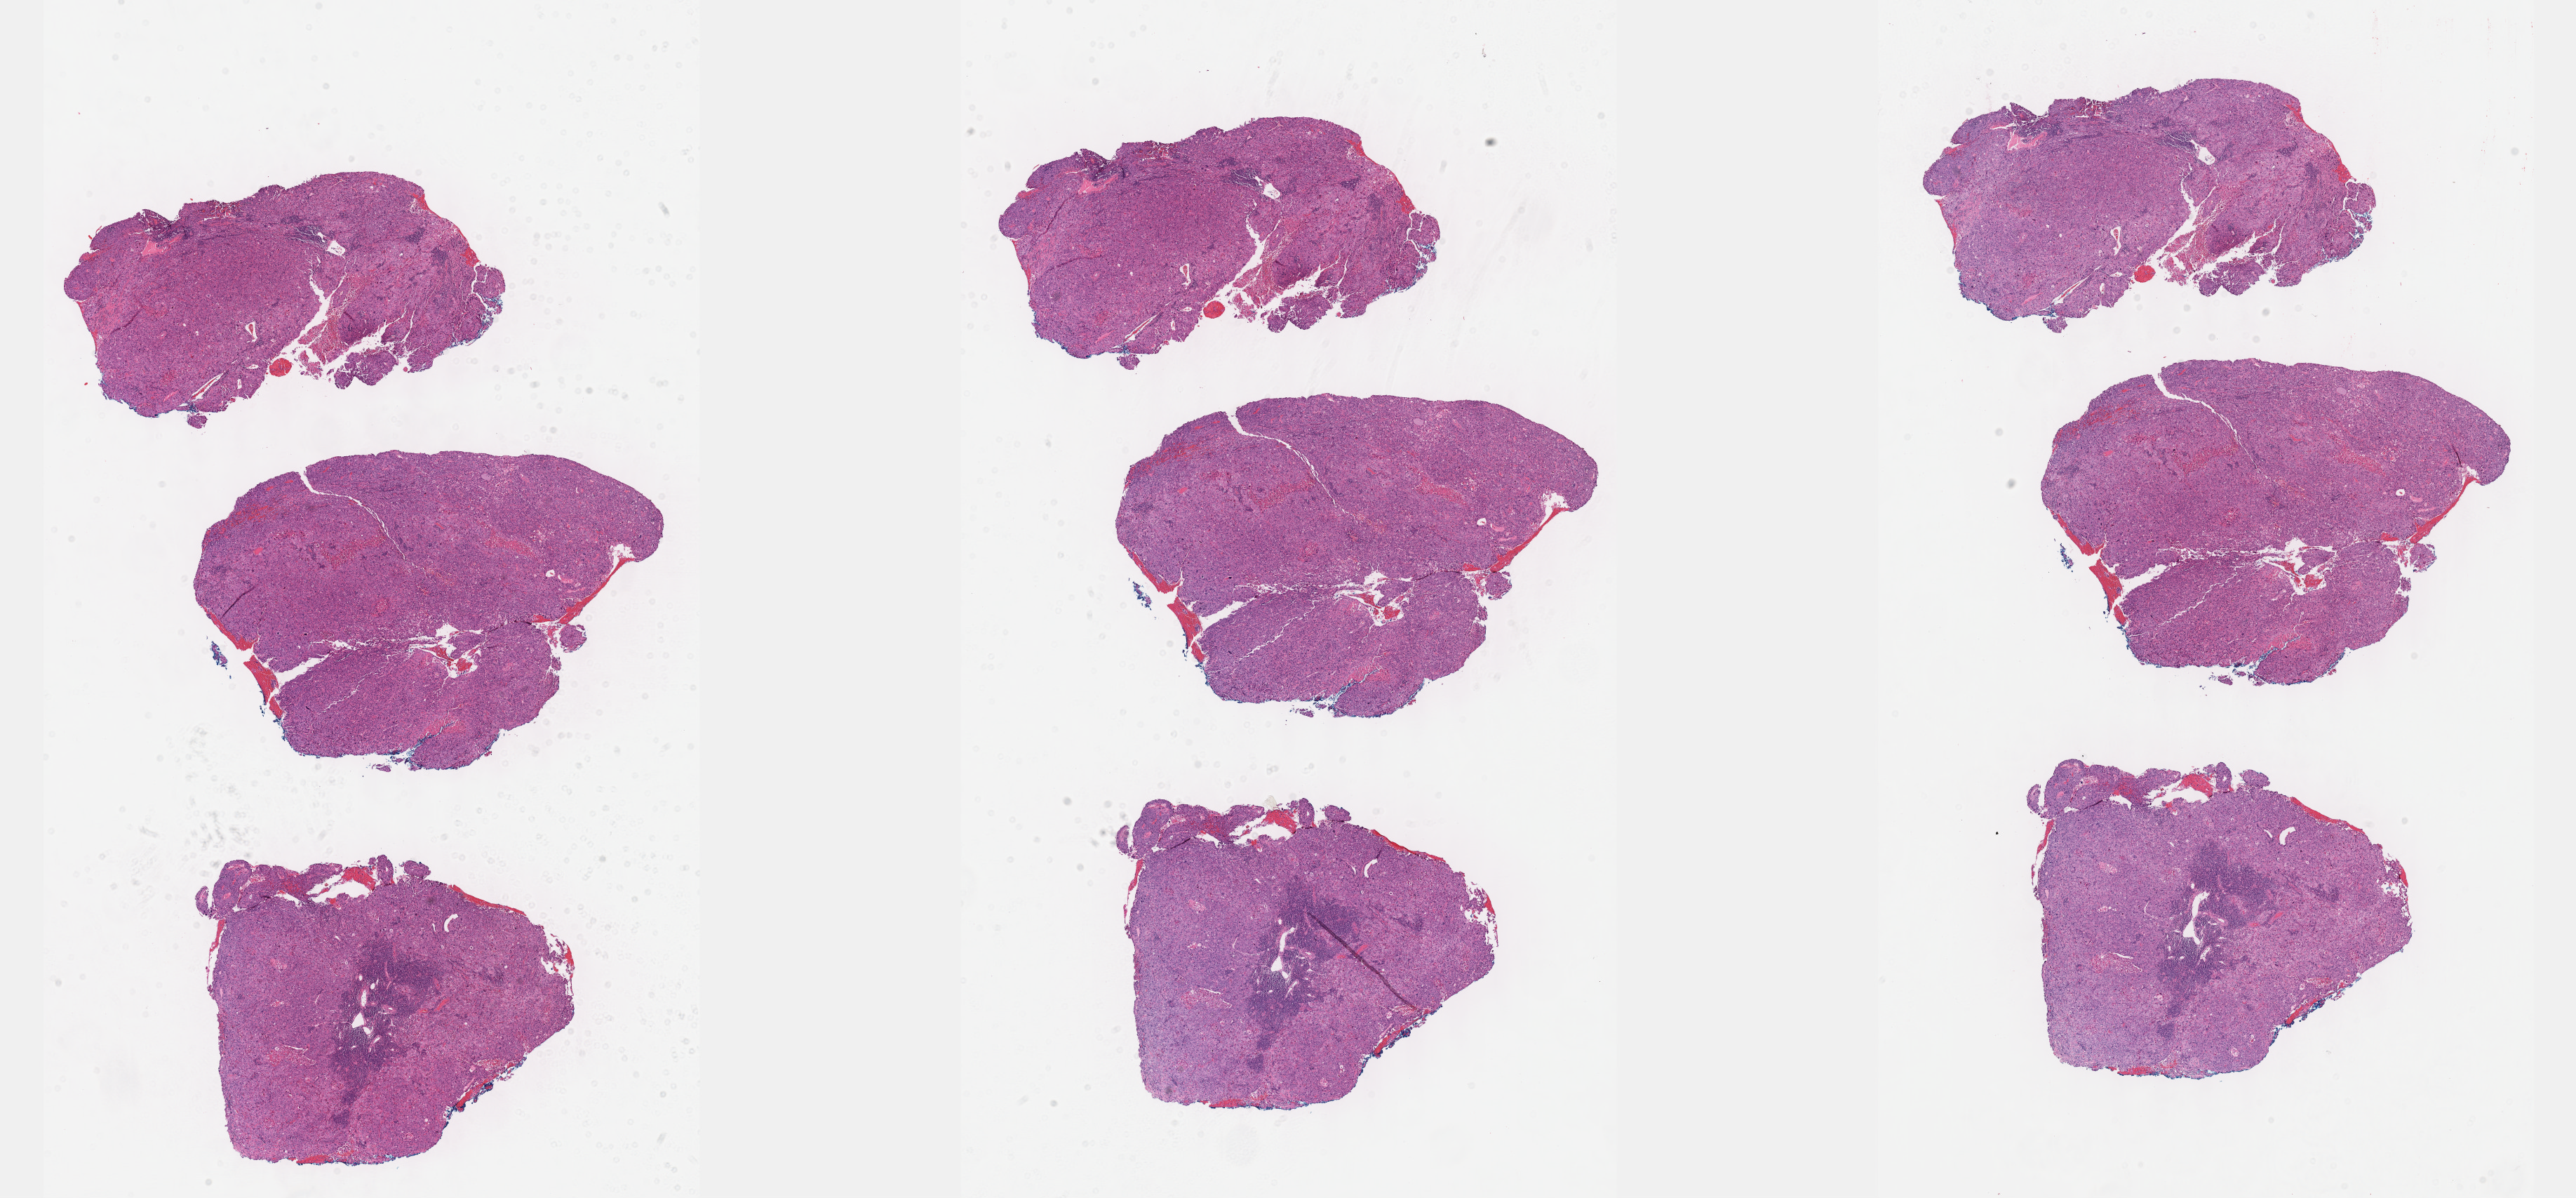
Digitized H&E tissue section (whole slide) — shown as a low-resolution overview of the whole scanned area (about 29.7 x 13.8 mm, acquisition: 40x scan); FFPE section; sample: primary tumour, cervix. Female patient; age at initial diagnosis 28 years. Histologic grade: G3 (poorly differentiated).
• FIGO stage: IIA
• pathologic diagnosis: Squamous cell carcinoma, NOS (cervix uteri)